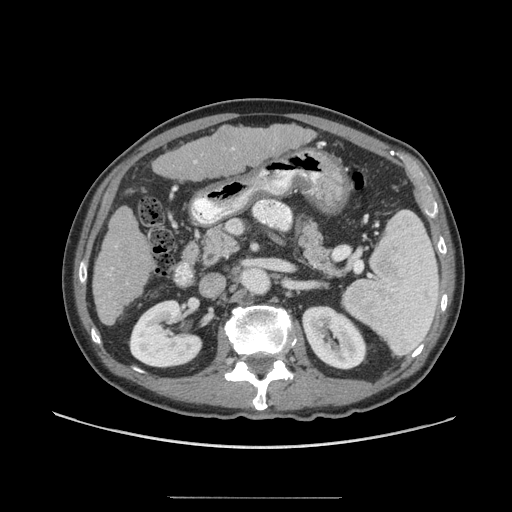
Contrast-enhanced abdominal CT (liver protocol), one axial slice. Slice 24 of 71 in the series (ordered by position). Reconstruction kernel STANDARD. 140 kVp. Soft-tissue window (W 400 / L 40 HU). 2.5 mm slice thickness. 512 × 512 image matrix, field of view 400 × 400 mm. Case-level facts recorded for this patient, not image findings: diagnosis: hepatocellular carcinoma (patient treated with transarterial chemoembolisation; whether this scan precedes or follows treatment is not stated here); TNM stage (as recorded): Stage-I; Child-Pugh class: A; tumour differentiation: well differentiated; tumour size: 3.5 cm.
Annotated regions visible in this slice (semi-automatically segmented with operator editing):
- liver parenchyma outside the tumour (the mass and vessels are separate outlines, so this box may not span the whole liver): bounding box (x1, y1, x2, y2) in pixels: (92, 124, 314, 325)
- liver vessels: (107, 148, 234, 276)